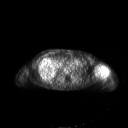
FDG PET of an extremity soft-tissue mass (from a PET/CT study), one axial slice. Slice 143 of 267 in the series (ordered by position). 3.27 mm slice thickness. 128 × 128 image matrix, field of view 700 × 700 mm. Female patient, age 83 years. Case-level facts recorded for this patient, not image findings: histological type: pleiomorphic leiomyosarcoma; grade: high; site of the primary tumour: left biceps.
Structures marked on this image (expert contour drawn on MRI and transferred to this co-registered scan by the dataset authors):
- gross tumour volume including surrounding oedema: box from (x=96, y=65) to (x=108, y=76) px
- gross tumour volume (mass): (x=96, y=65)–(x=108, y=74)